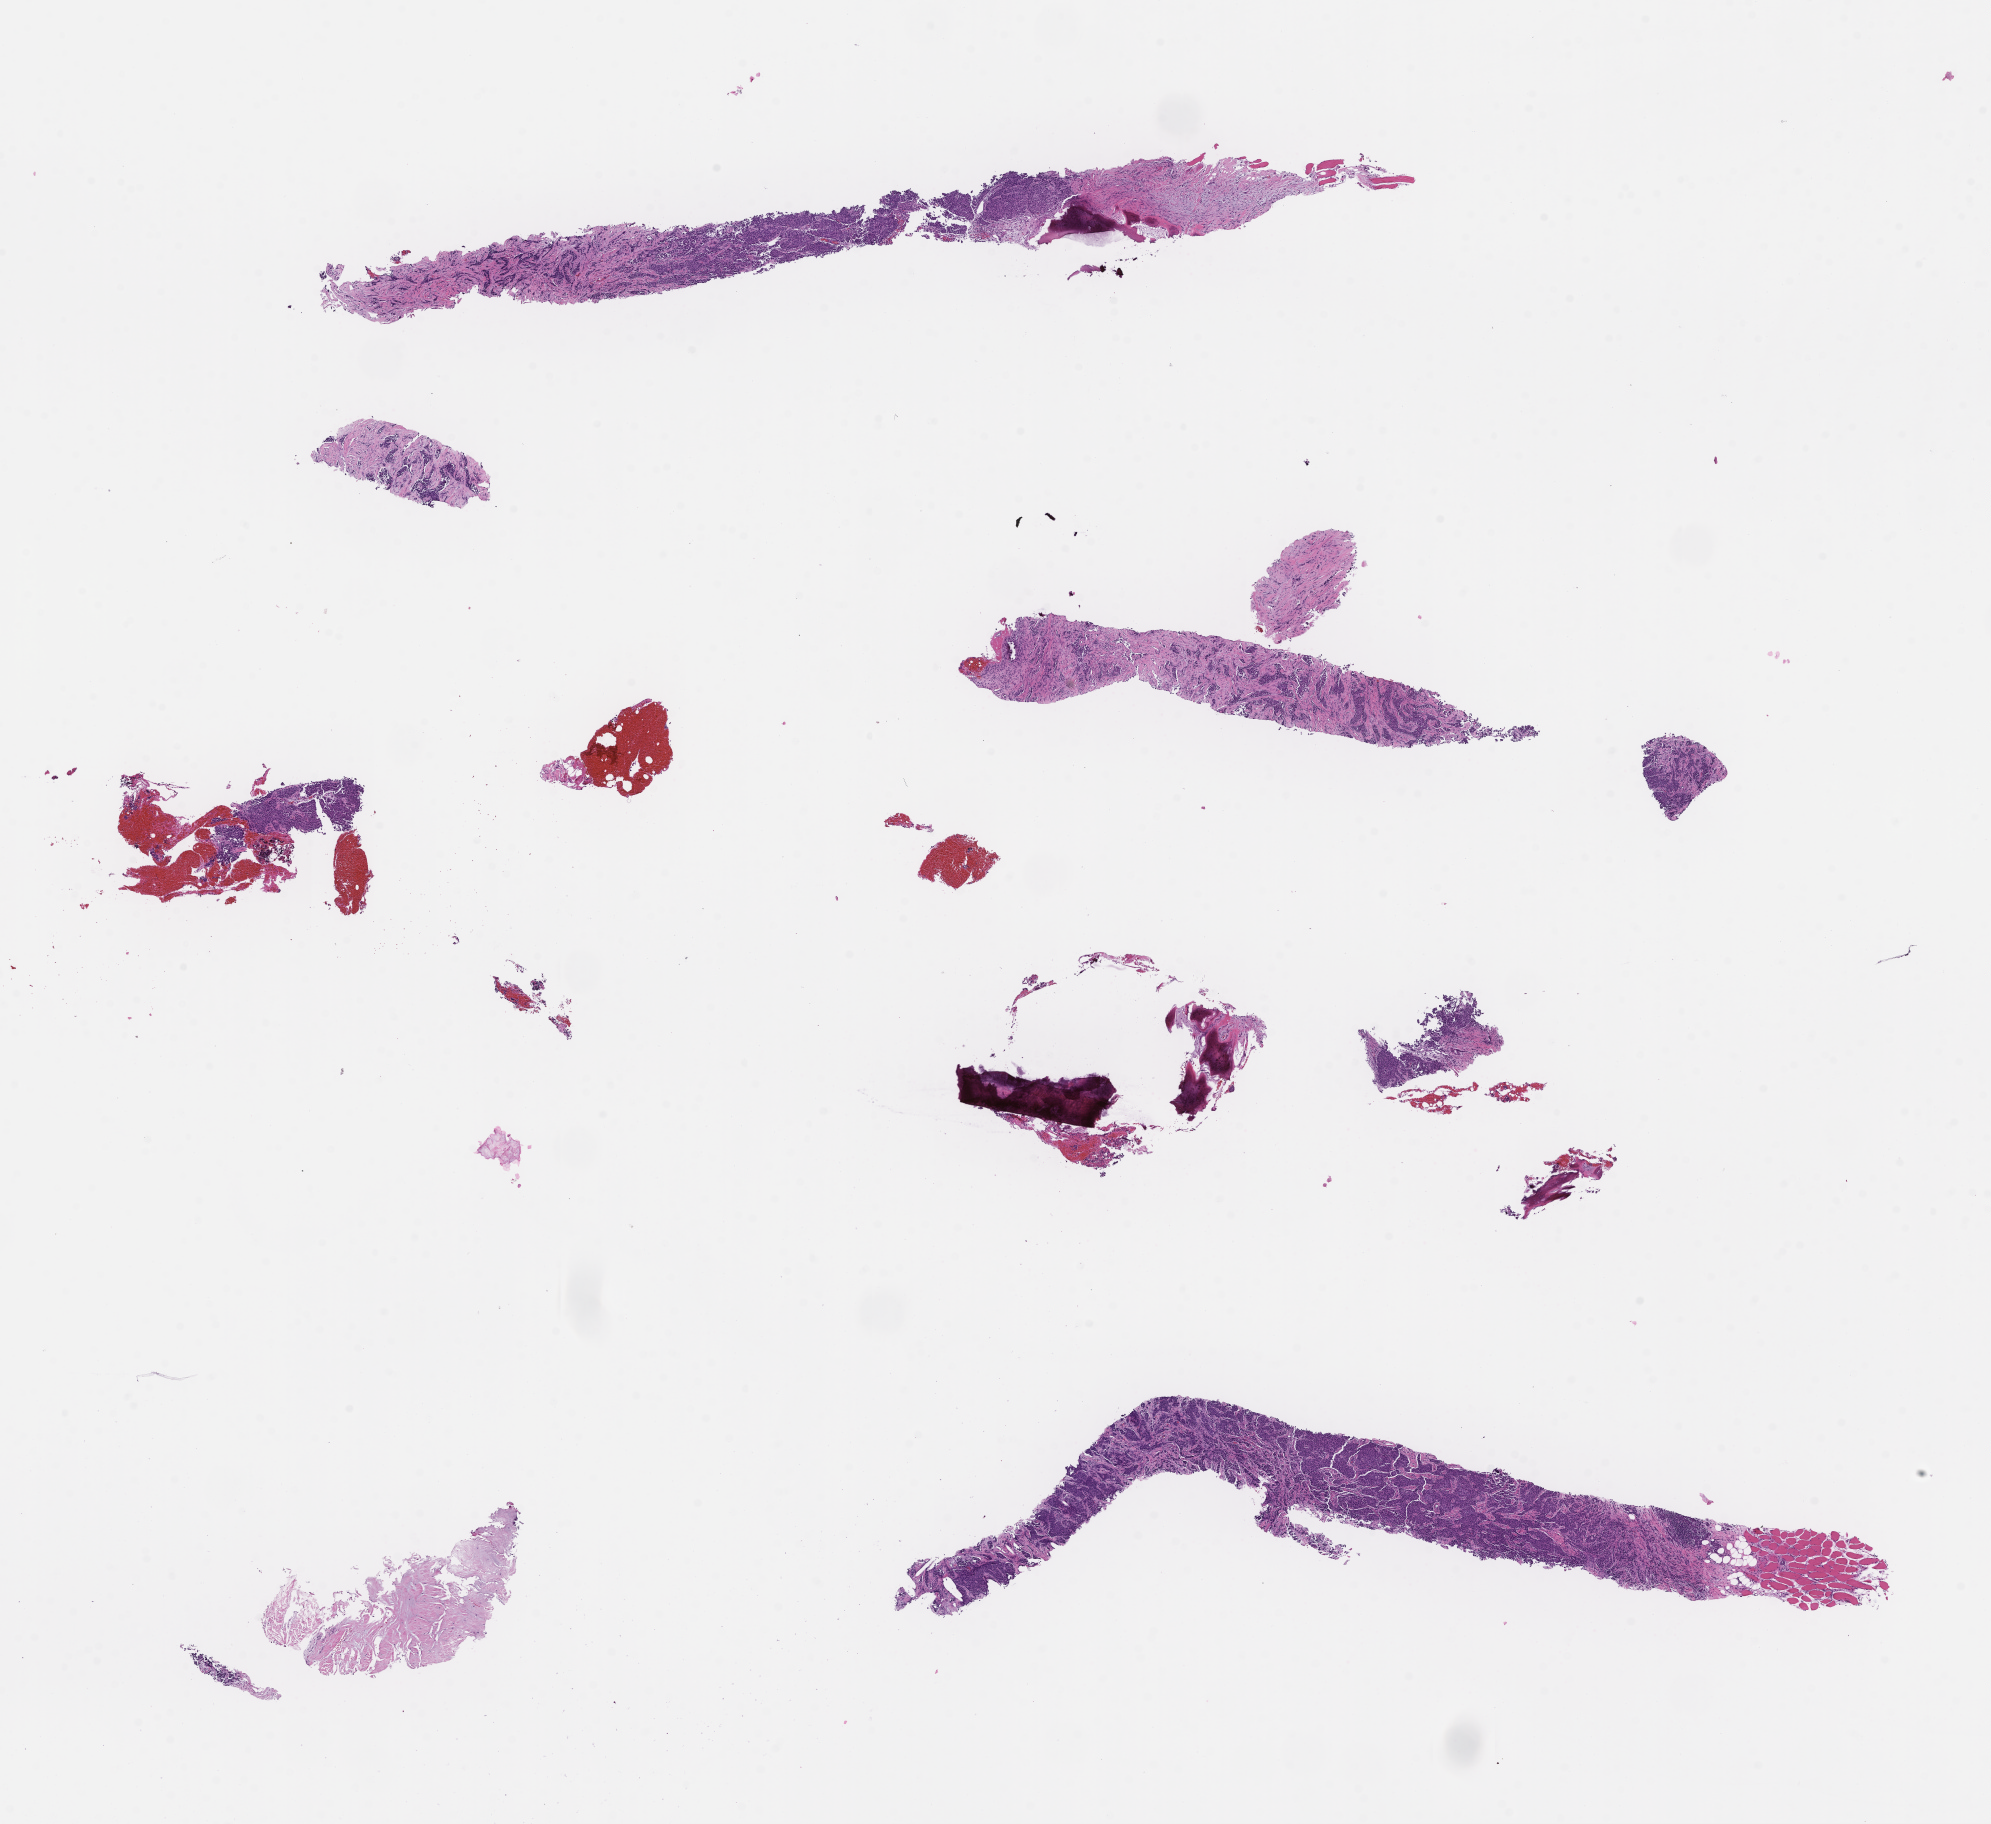
Digitized haematoxylin and eosin-stained section, low-resolution overview of the scanned area, about 16.1 x 14.7 mm; formalin-fixed, paraffin-embedded (FFPE) tissue. Patient sex: female.
This section: metastasis (sampled organ not recorded). Primary diagnosis of the patient: Invasive Breast Carcinoma.